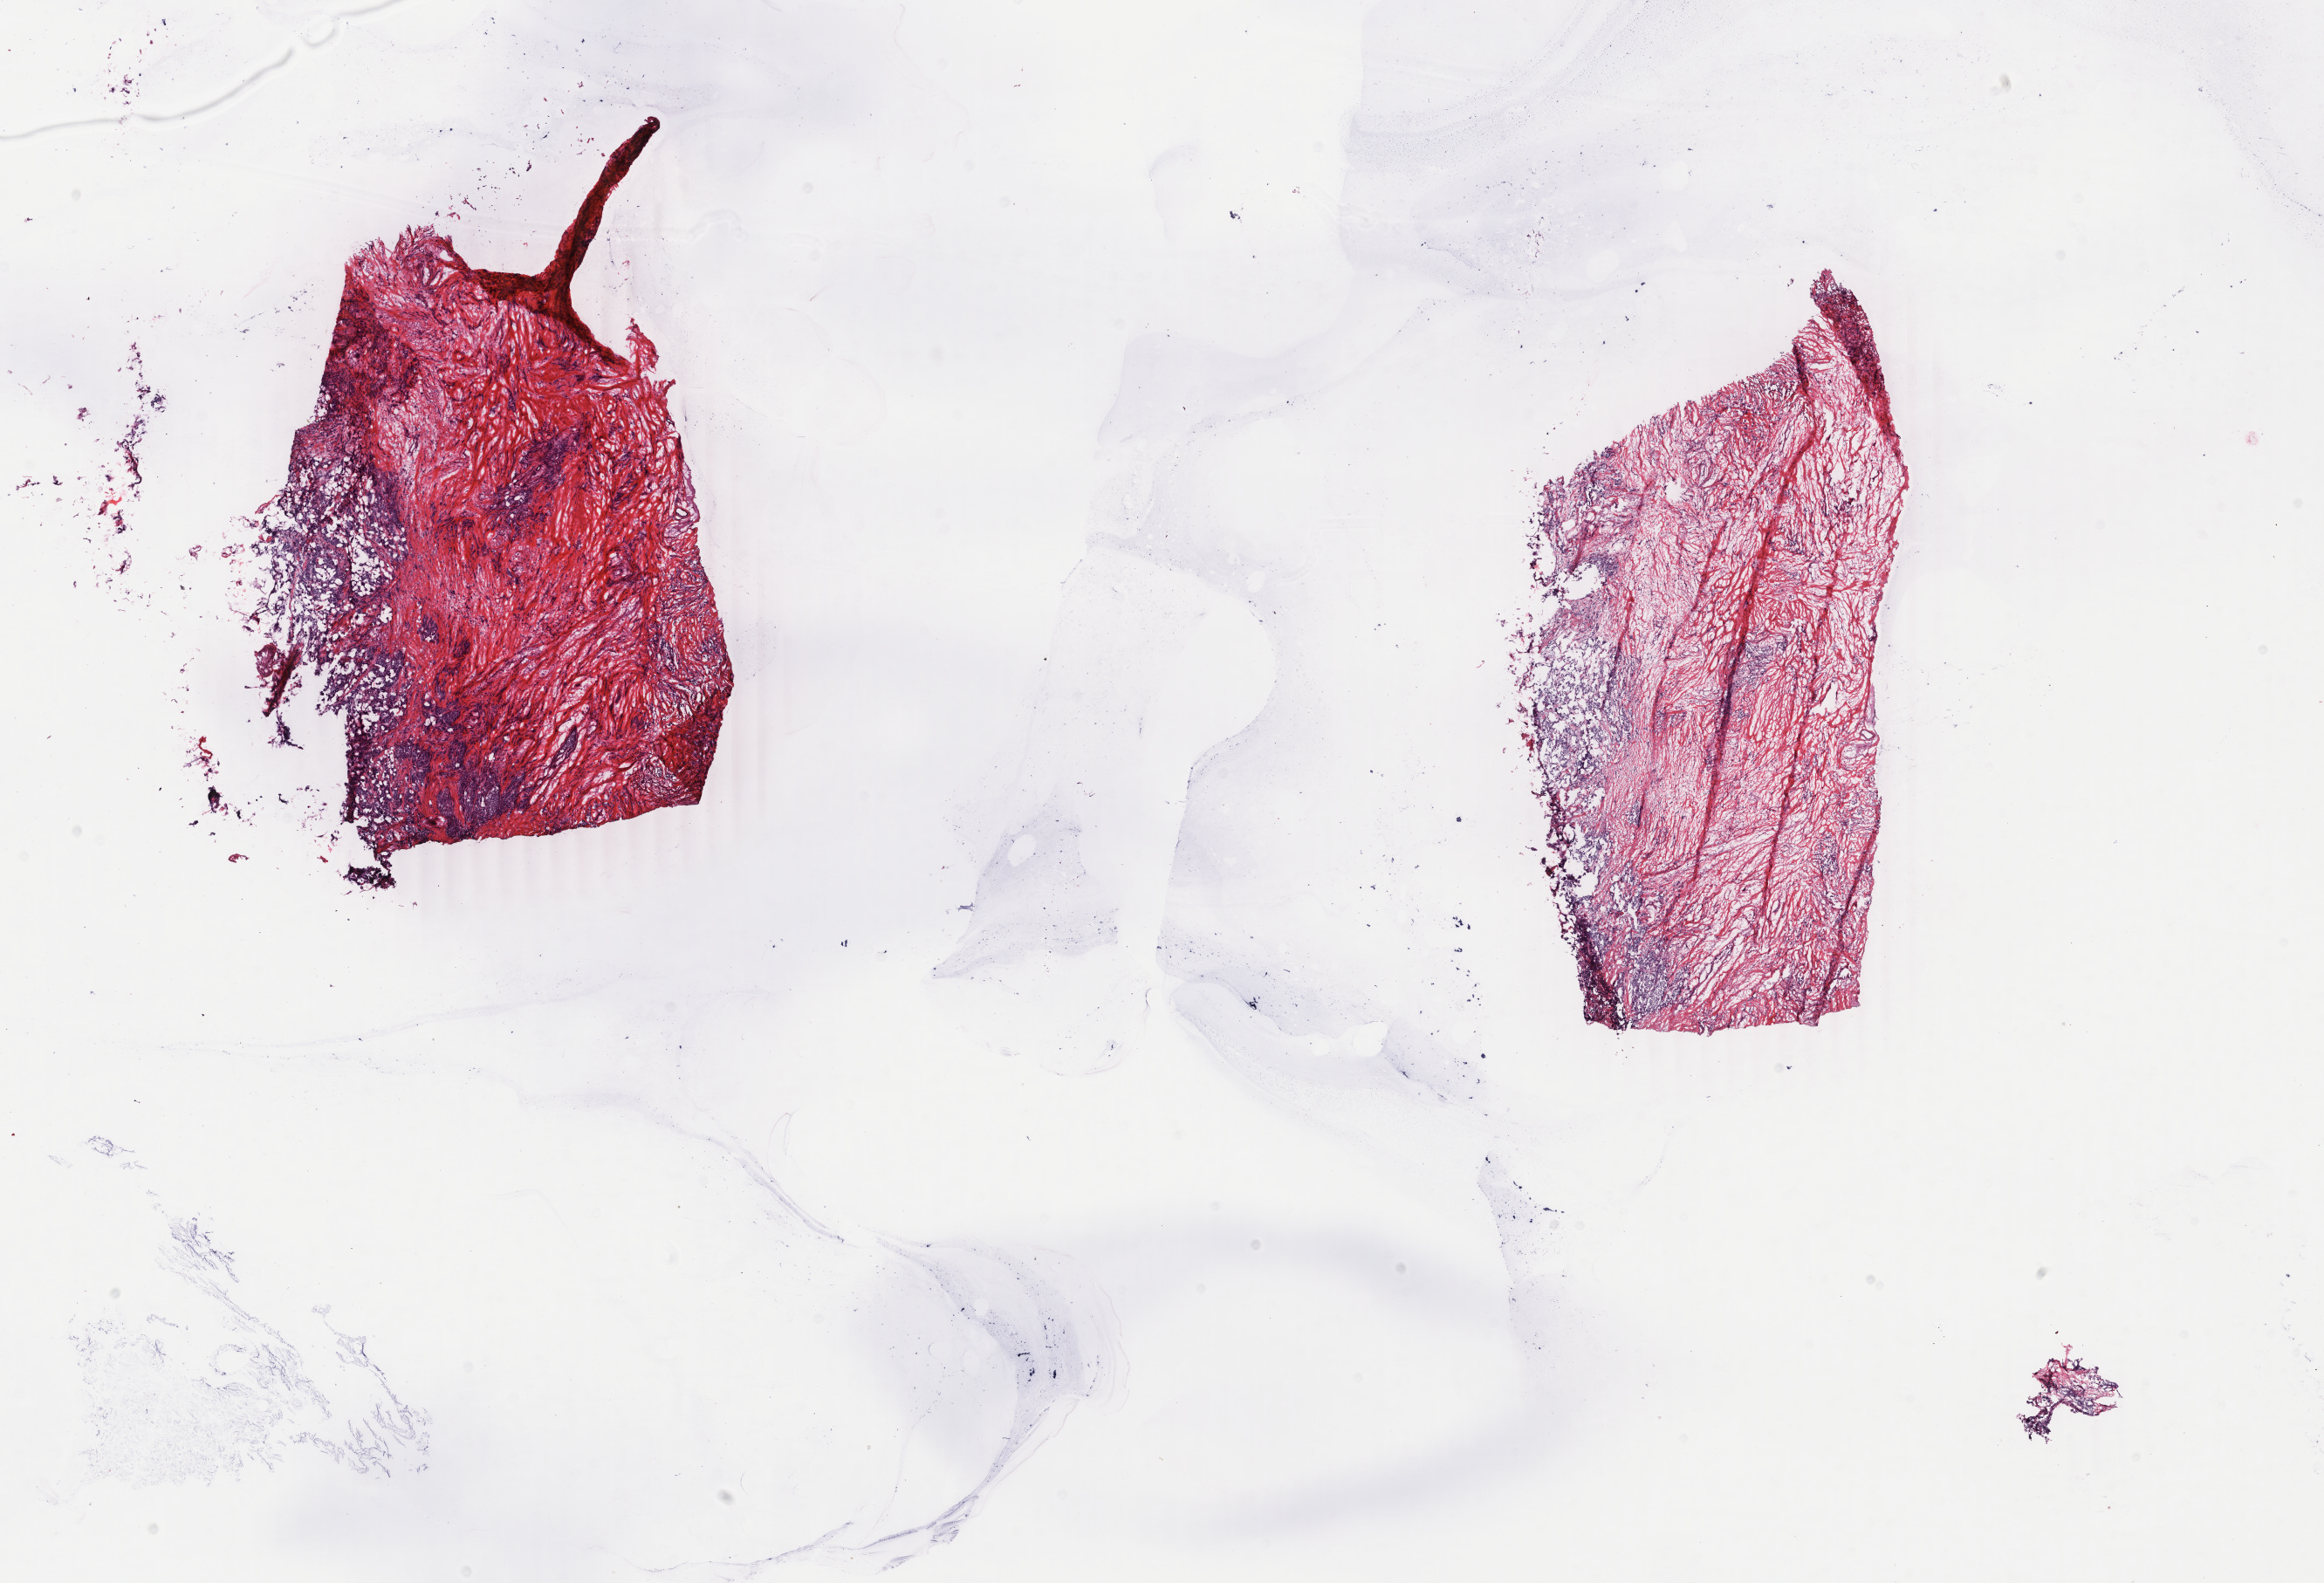
Whole-slide histology image, H&E-stained — low-resolution overview of the scanned area, about 21.2 x 14.4 mm (acquisition: 40x scan). Frozen section from the top of the tissue portion. Breast, primary tumour sample. Patient: female, age at initial diagnosis 62 years. Pathologist review of this section (percent, as recorded): tumour cells 70%, tumour nuclei 70%, normal cells 0%, stromal cells 28%, necrosis 2%. Infiltration values recorded for this section: lymphocyte infiltration 3%, monocyte infiltration 0%, neutrophil infiltration 0%.
Histologic diagnosis: Lobular carcinoma, NOS. AJCC pathologic stage: IIIA. Lymph nodes positive (case pathology): 1 of 14 examined.